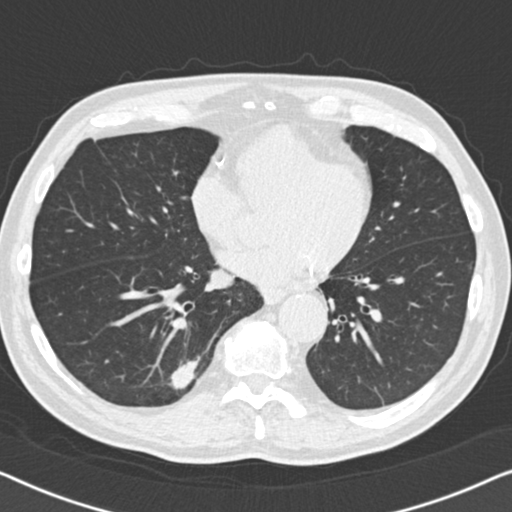
Low-dose screening chest CT, one axial slice. Position 55 of 164 along the scan axis. 120 kVp. Lung window (W 1500 / L -600 HU). 2 mm slice thickness. 512 × 512 image matrix, field of view 330 × 330 mm.
Structures marked on this image (expert manual segmentation):
- lesion 1 (tumor, lower lobe of right lung): bounding box [x1, y1, x2, y2] px = [168, 356, 201, 389]